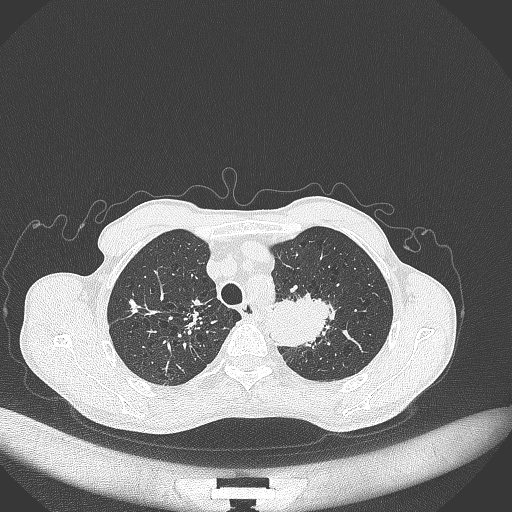
Chest CT, one axial slice; slice 344 of 386 in the series (ordered by position); 120 kVp; lung window (W 1500 / L -600 HU); 1 mm slice thickness; 512 × 512 image matrix. Patient: male, 65 years. Case-level facts recorded for this patient, not image findings: clinical TNM (as recorded): T2b N0 M0; histopathological grade: G2.
Outlined on this slice (bounding box drawn by a radiologist):
- lung tumour (recorded histology: adenocarcinoma): bounding box <272,286,335,349> (left, top, right, bottom; pixels)